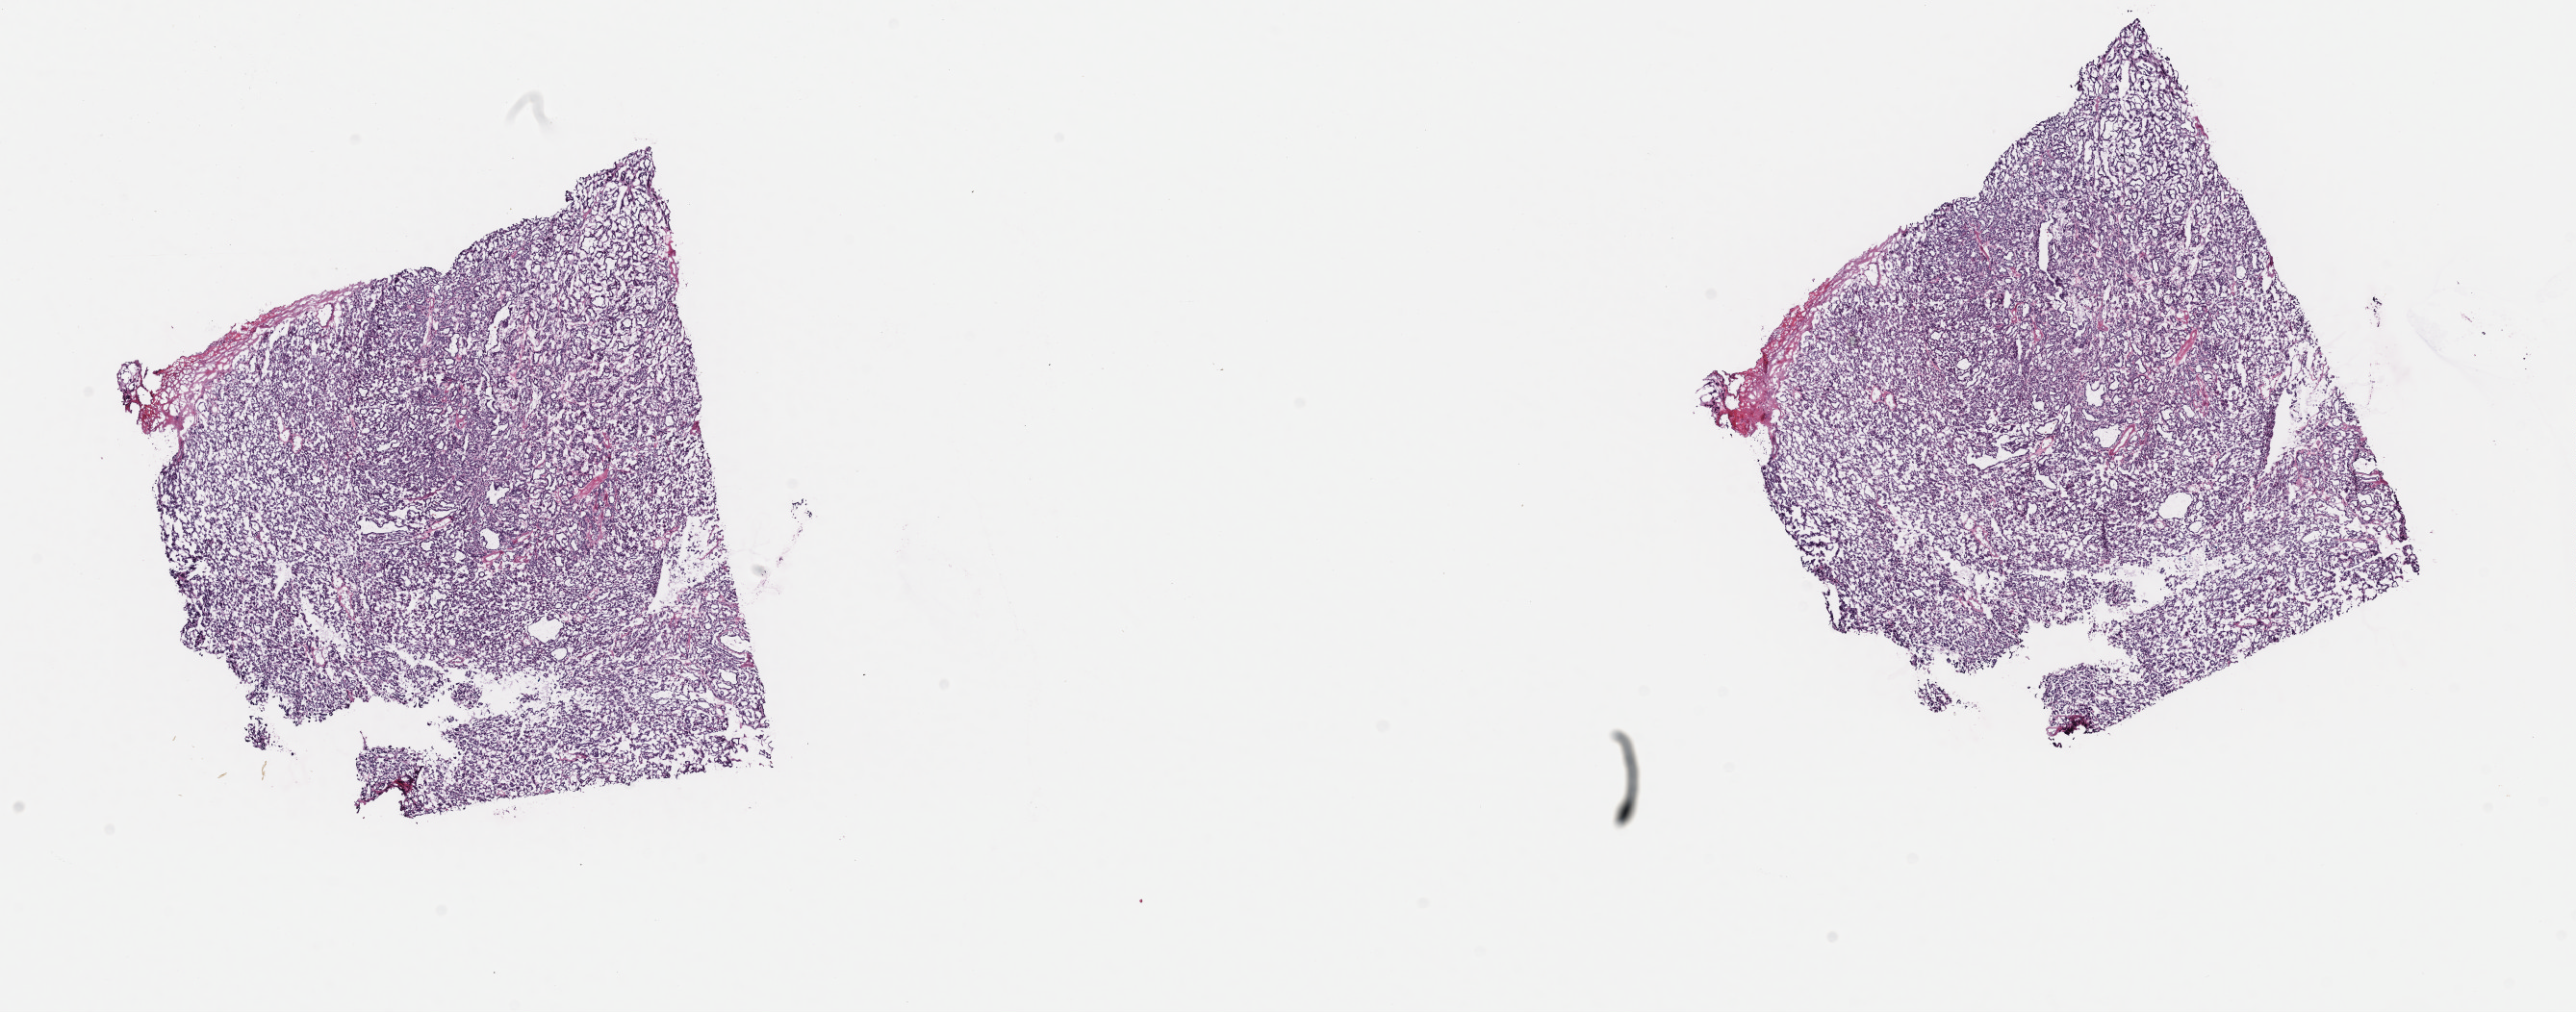
Digitized H&E tissue section (whole slide), low-resolution overview of the scanned area, about 21.1 x 8.3 mm (from a 40x scan), frozen section from the top of the tissue portion, primary tumour sample from the thyroid. Patient: male, age at initial diagnosis 70 years. Slide review estimates, as recorded: tumour cells 100%, tumour nuclei 95%.
Histologic diagnosis: Papillary carcinoma, follicular variant (thyroid gland).